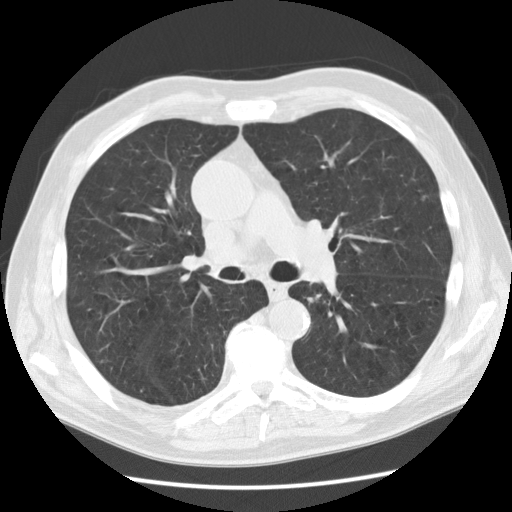
Chest CT (low-dose screening protocol), one axial image, second annual screen, lung window (W 1500 / L -600 HU), standard (soft-tissue) reconstruction kernel (STANDARD). Male, age 73 years at enrolment. Current smoker at enrolment.
• Expert reader's lesion annotation, box from (x=294, y=277) to (x=338, y=318) px.
• The screening reader recorded 4 non-calcified nodules or masses ≥4 mm on this exam (right upper lobe, right upper lobe, left upper lobe, right lower lobe); which of them this box marks is not recorded.
• Official screen result: positive, no significant change: stable abnormalities potentially related to lung cancer, unchanged since the prior screening exam.
• Participant outcome: lung cancer diagnosed 302 days after this screen — small cell carcinoma, NOS, left lower lobe, stage IIIB (AJCC 6th edition), 55 mm at pathology.